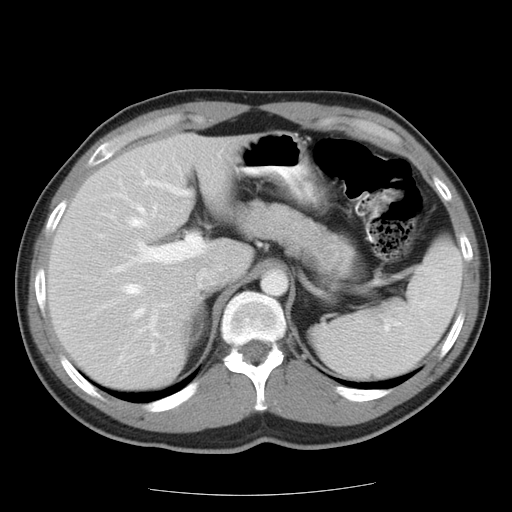
Contrast-enhanced abdominal CT, one axial slice; slice 13 of 22 in the series (ordered by position); reconstruction kernel STANDARD; intravenous contrast given; soft-tissue window (W 400 / L 40 HU); 512 × 512 image matrix. Male patient, age 41 years. From the clinical record (not read from this slice): diagnosis: colorectal cancer liver metastases, imaged before liver resection; multiple liver metastases: no; largest metastasis: 2.7 cm; disease in both lobes: no.
Outlined on this slice (manually delineated by an expert):
- hepatic veins: bounding box (x1, y1, x2, y2) in pixels: (127, 207, 145, 317)
- liver: (49, 137, 248, 386)
- planned liver remnant (the part of the liver to remain after resection): (49, 137, 247, 347)
- portal vein (with intrahepatic branches): (114, 180, 208, 321)
- liver metastasis: (162, 343, 177, 355)